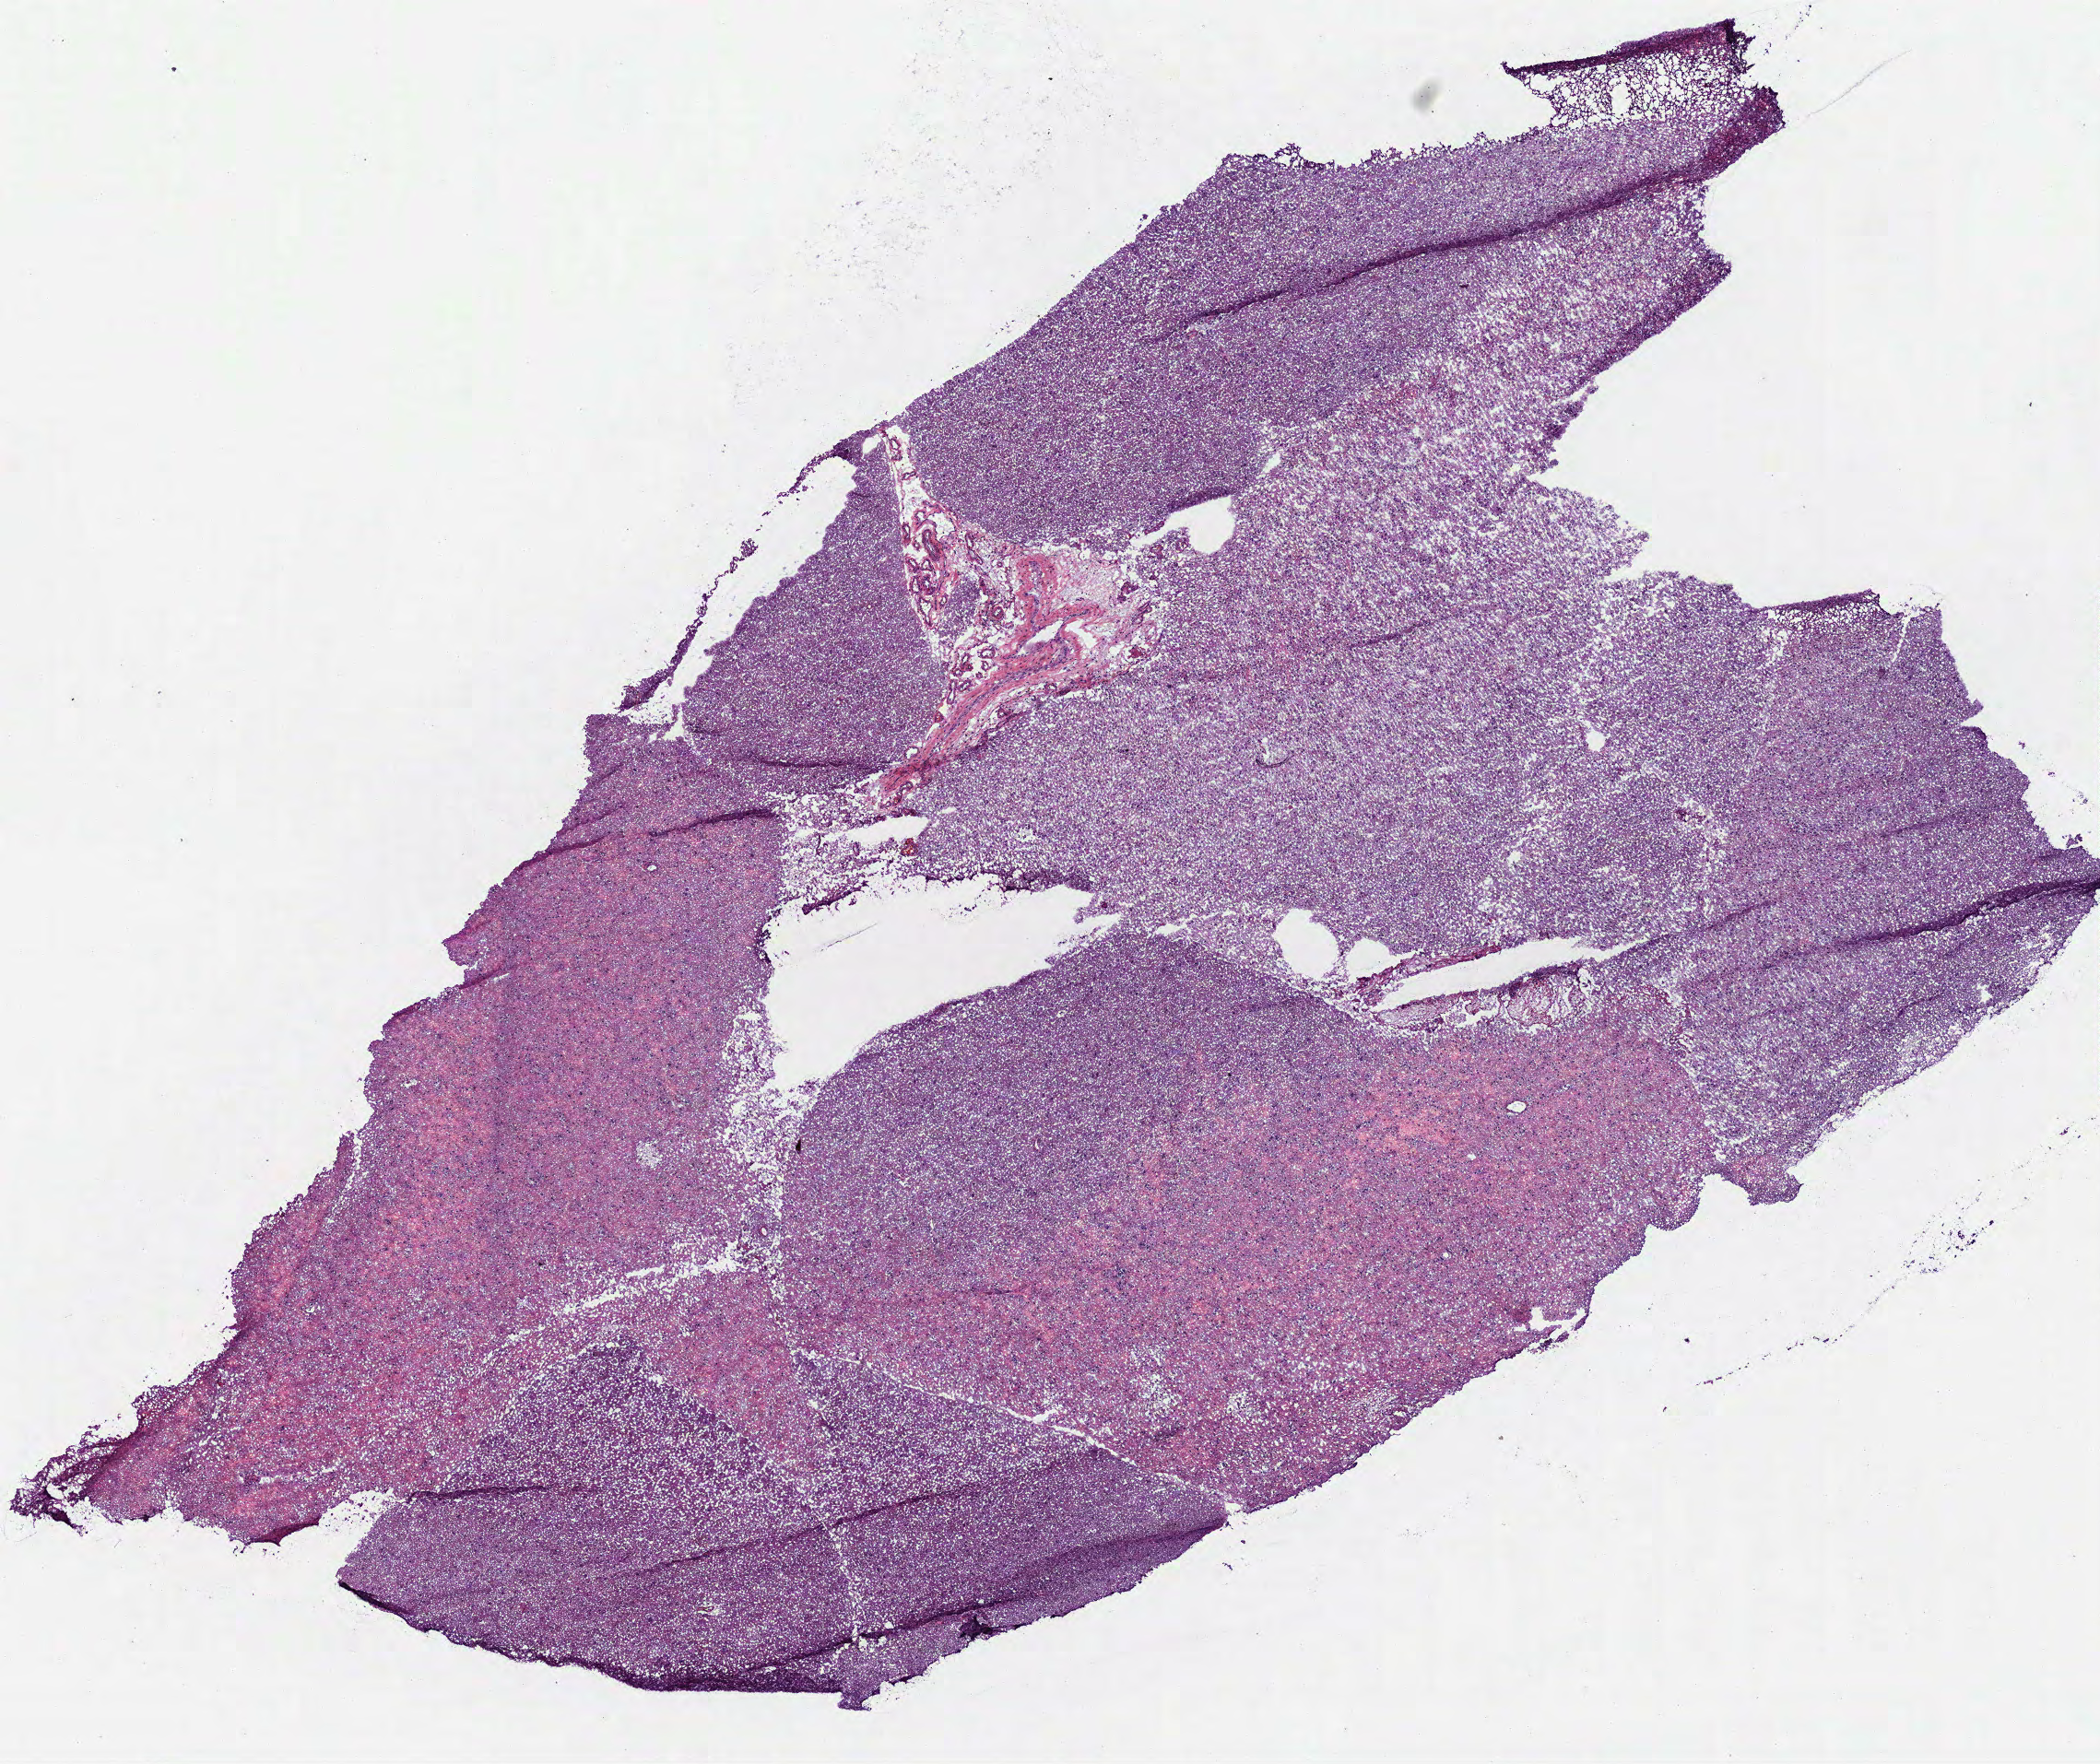
Digitized H&E-stained tissue section (whole slide) — a low-resolution overview of the entire scanned area, about 9.2 x 7.7 mm. Frozen section. Sample: primary tumour, brain. Female, age 20 years at initial diagnosis. Histologic grade: G2 (moderately differentiated). Pathologist review of this section (percent, as recorded): tumour cells 95%, tumour nuclei 70%, normal cells 5%, stromal cells 0%, necrosis 0%.
Pathologic diagnosis: Oligodendroglioma, NOS (cerebrum).